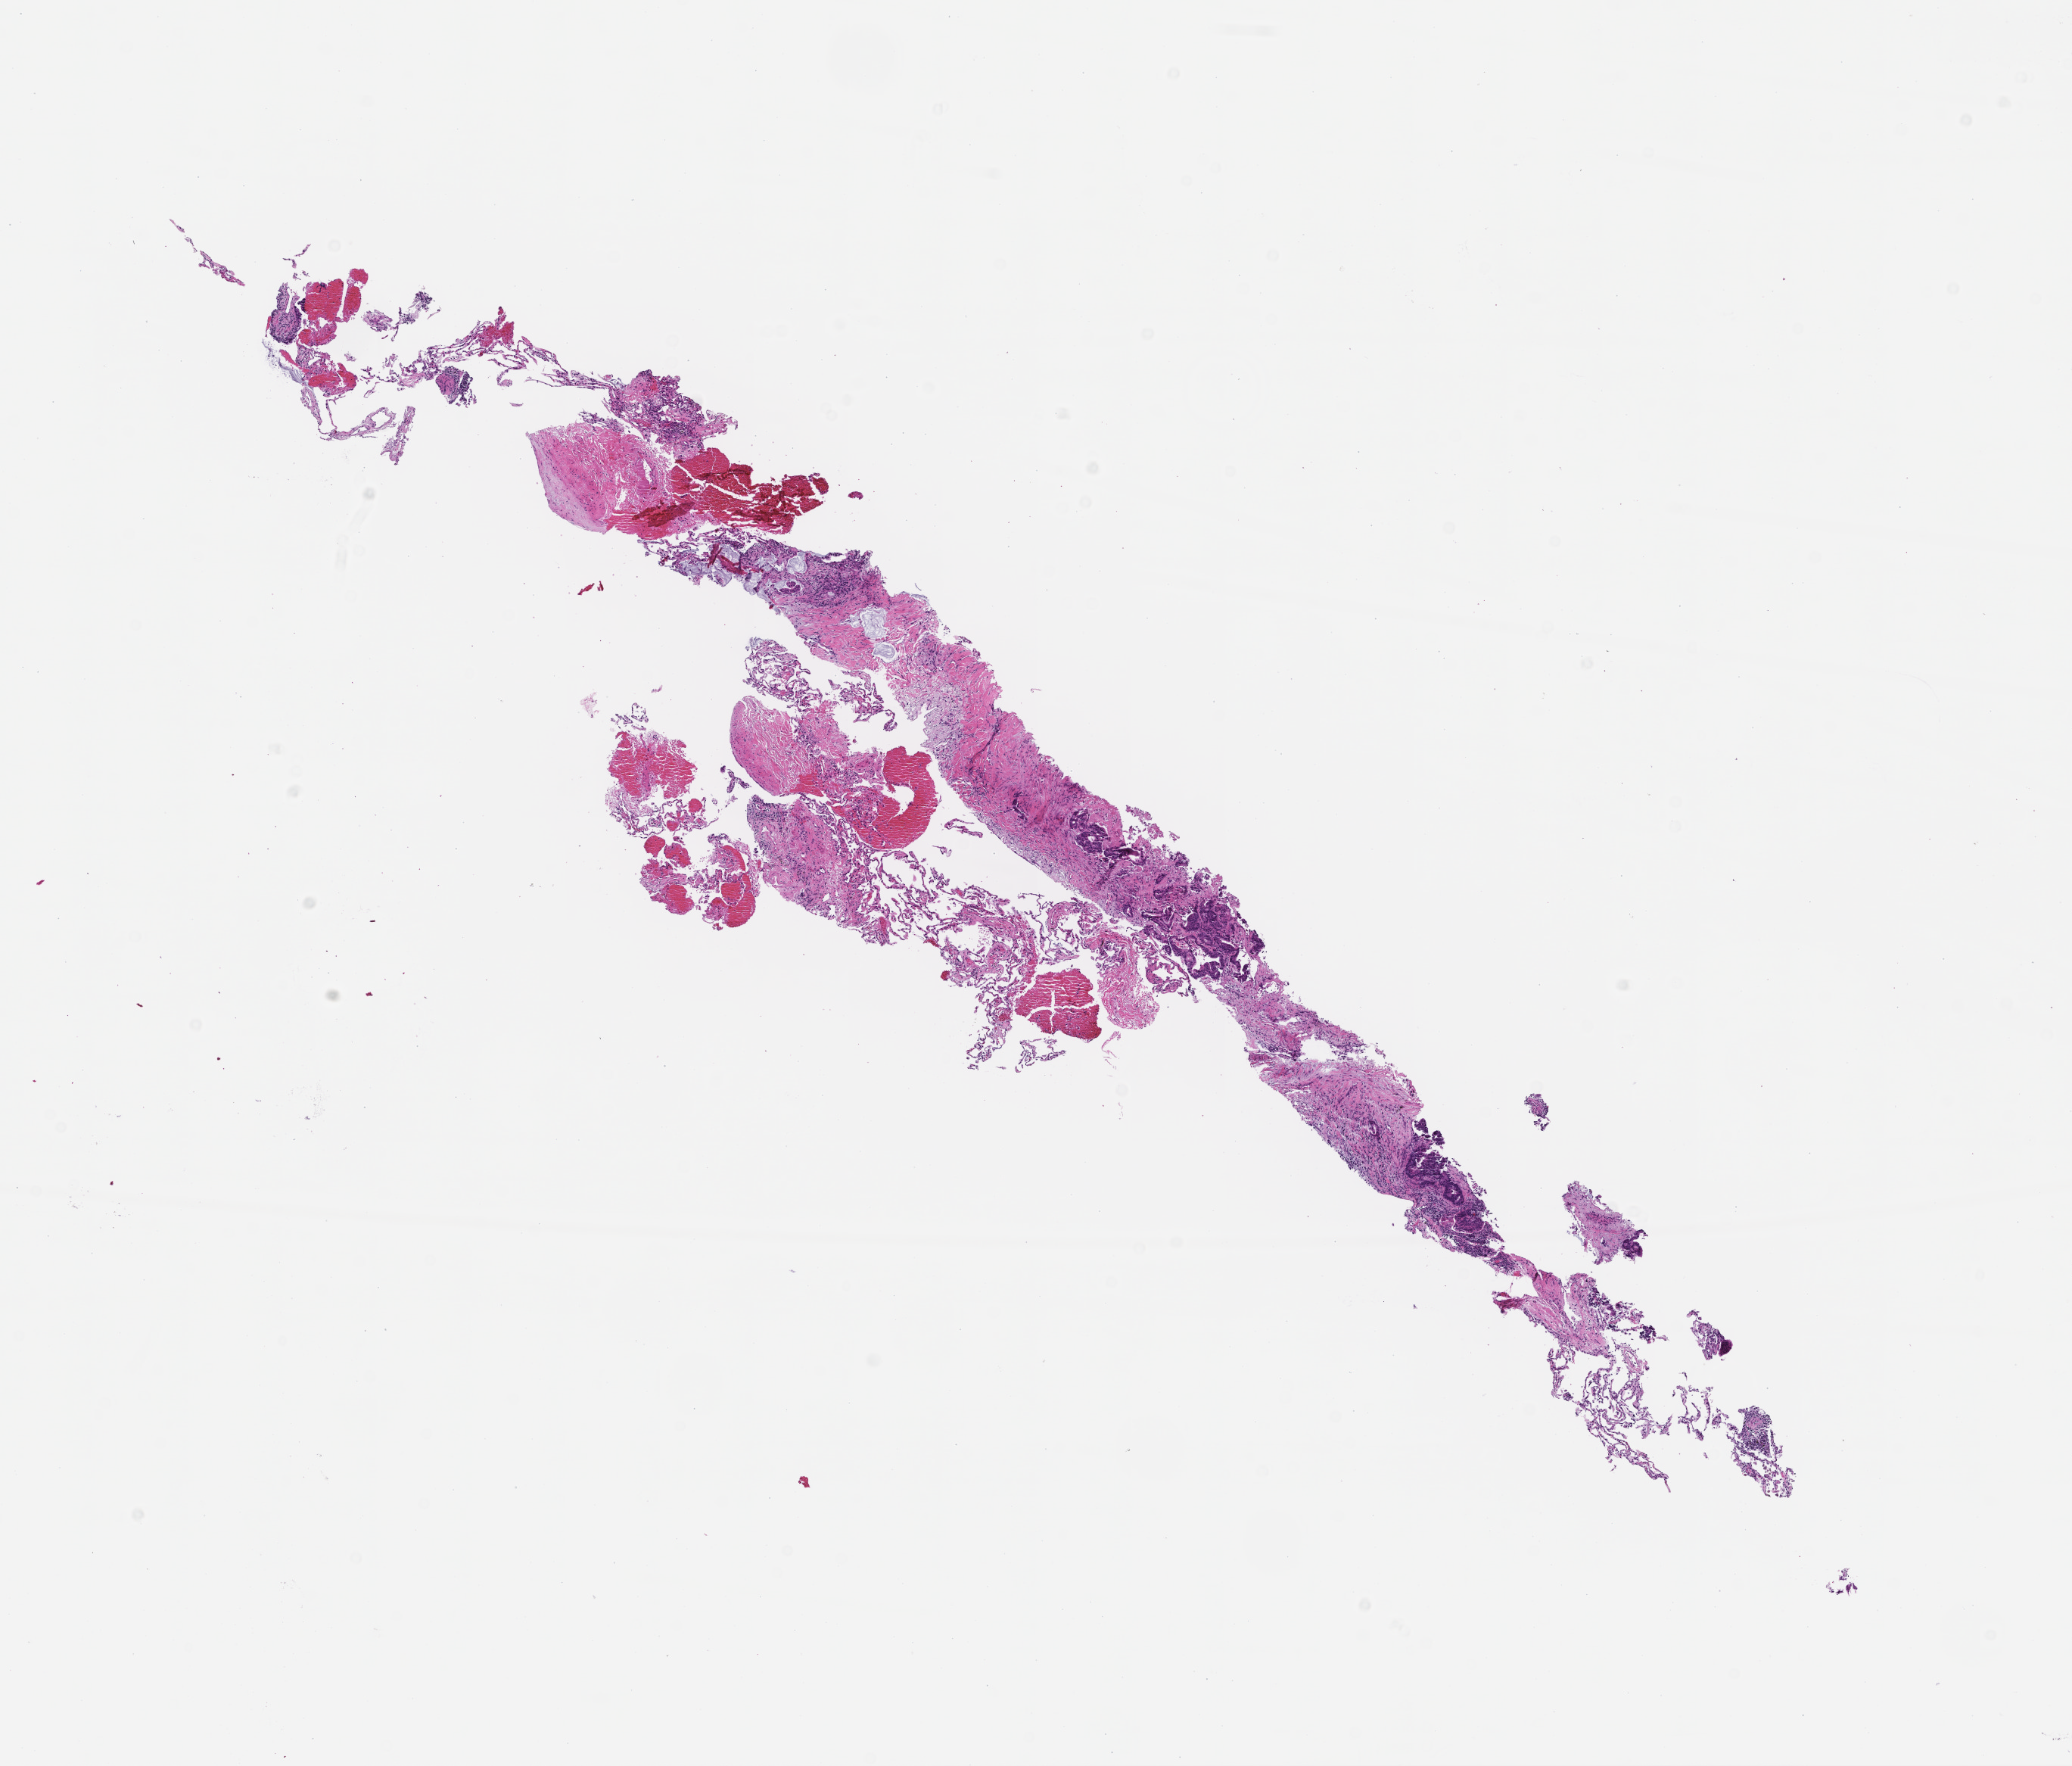
Whole-slide image, hematoxylin and eosin (H&E) stain, low-resolution overview of the scanned area, about 11.1 x 9.4 mm, FFPE section. Male patient.
This section: metastasis (sampled organ not recorded). Patient diagnosis (primary): Colorectal Carcinoma.